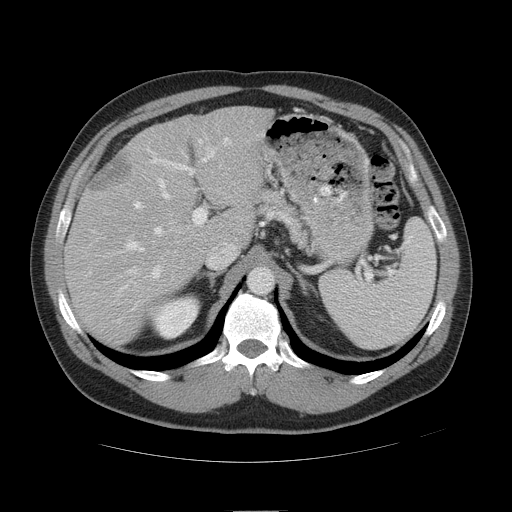
Contrast-enhanced abdominal CT, one axial slice. Intravenous contrast given. Soft-tissue window (W 400 / L 40 HU). 512 × 512 image matrix. Male patient, age 52 years. From the clinical record (not read from this slice): diagnosis: colorectal cancer liver metastases, imaged before liver resection; multiple liver metastases: yes; largest metastasis: 5.1 cm.
Outlined on this slice (manually delineated by an expert):
- hepatic veins: box from (x=126, y=139) to (x=203, y=273) px
- liver: (x=67, y=108)–(x=268, y=344)
- planned liver remnant (the part of the liver to remain after resection): (x=135, y=108)–(x=268, y=240)
- portal vein (with intrahepatic branches): (x=118, y=137)–(x=229, y=296)
- liver metastasis: (x=90, y=154)–(x=134, y=195)